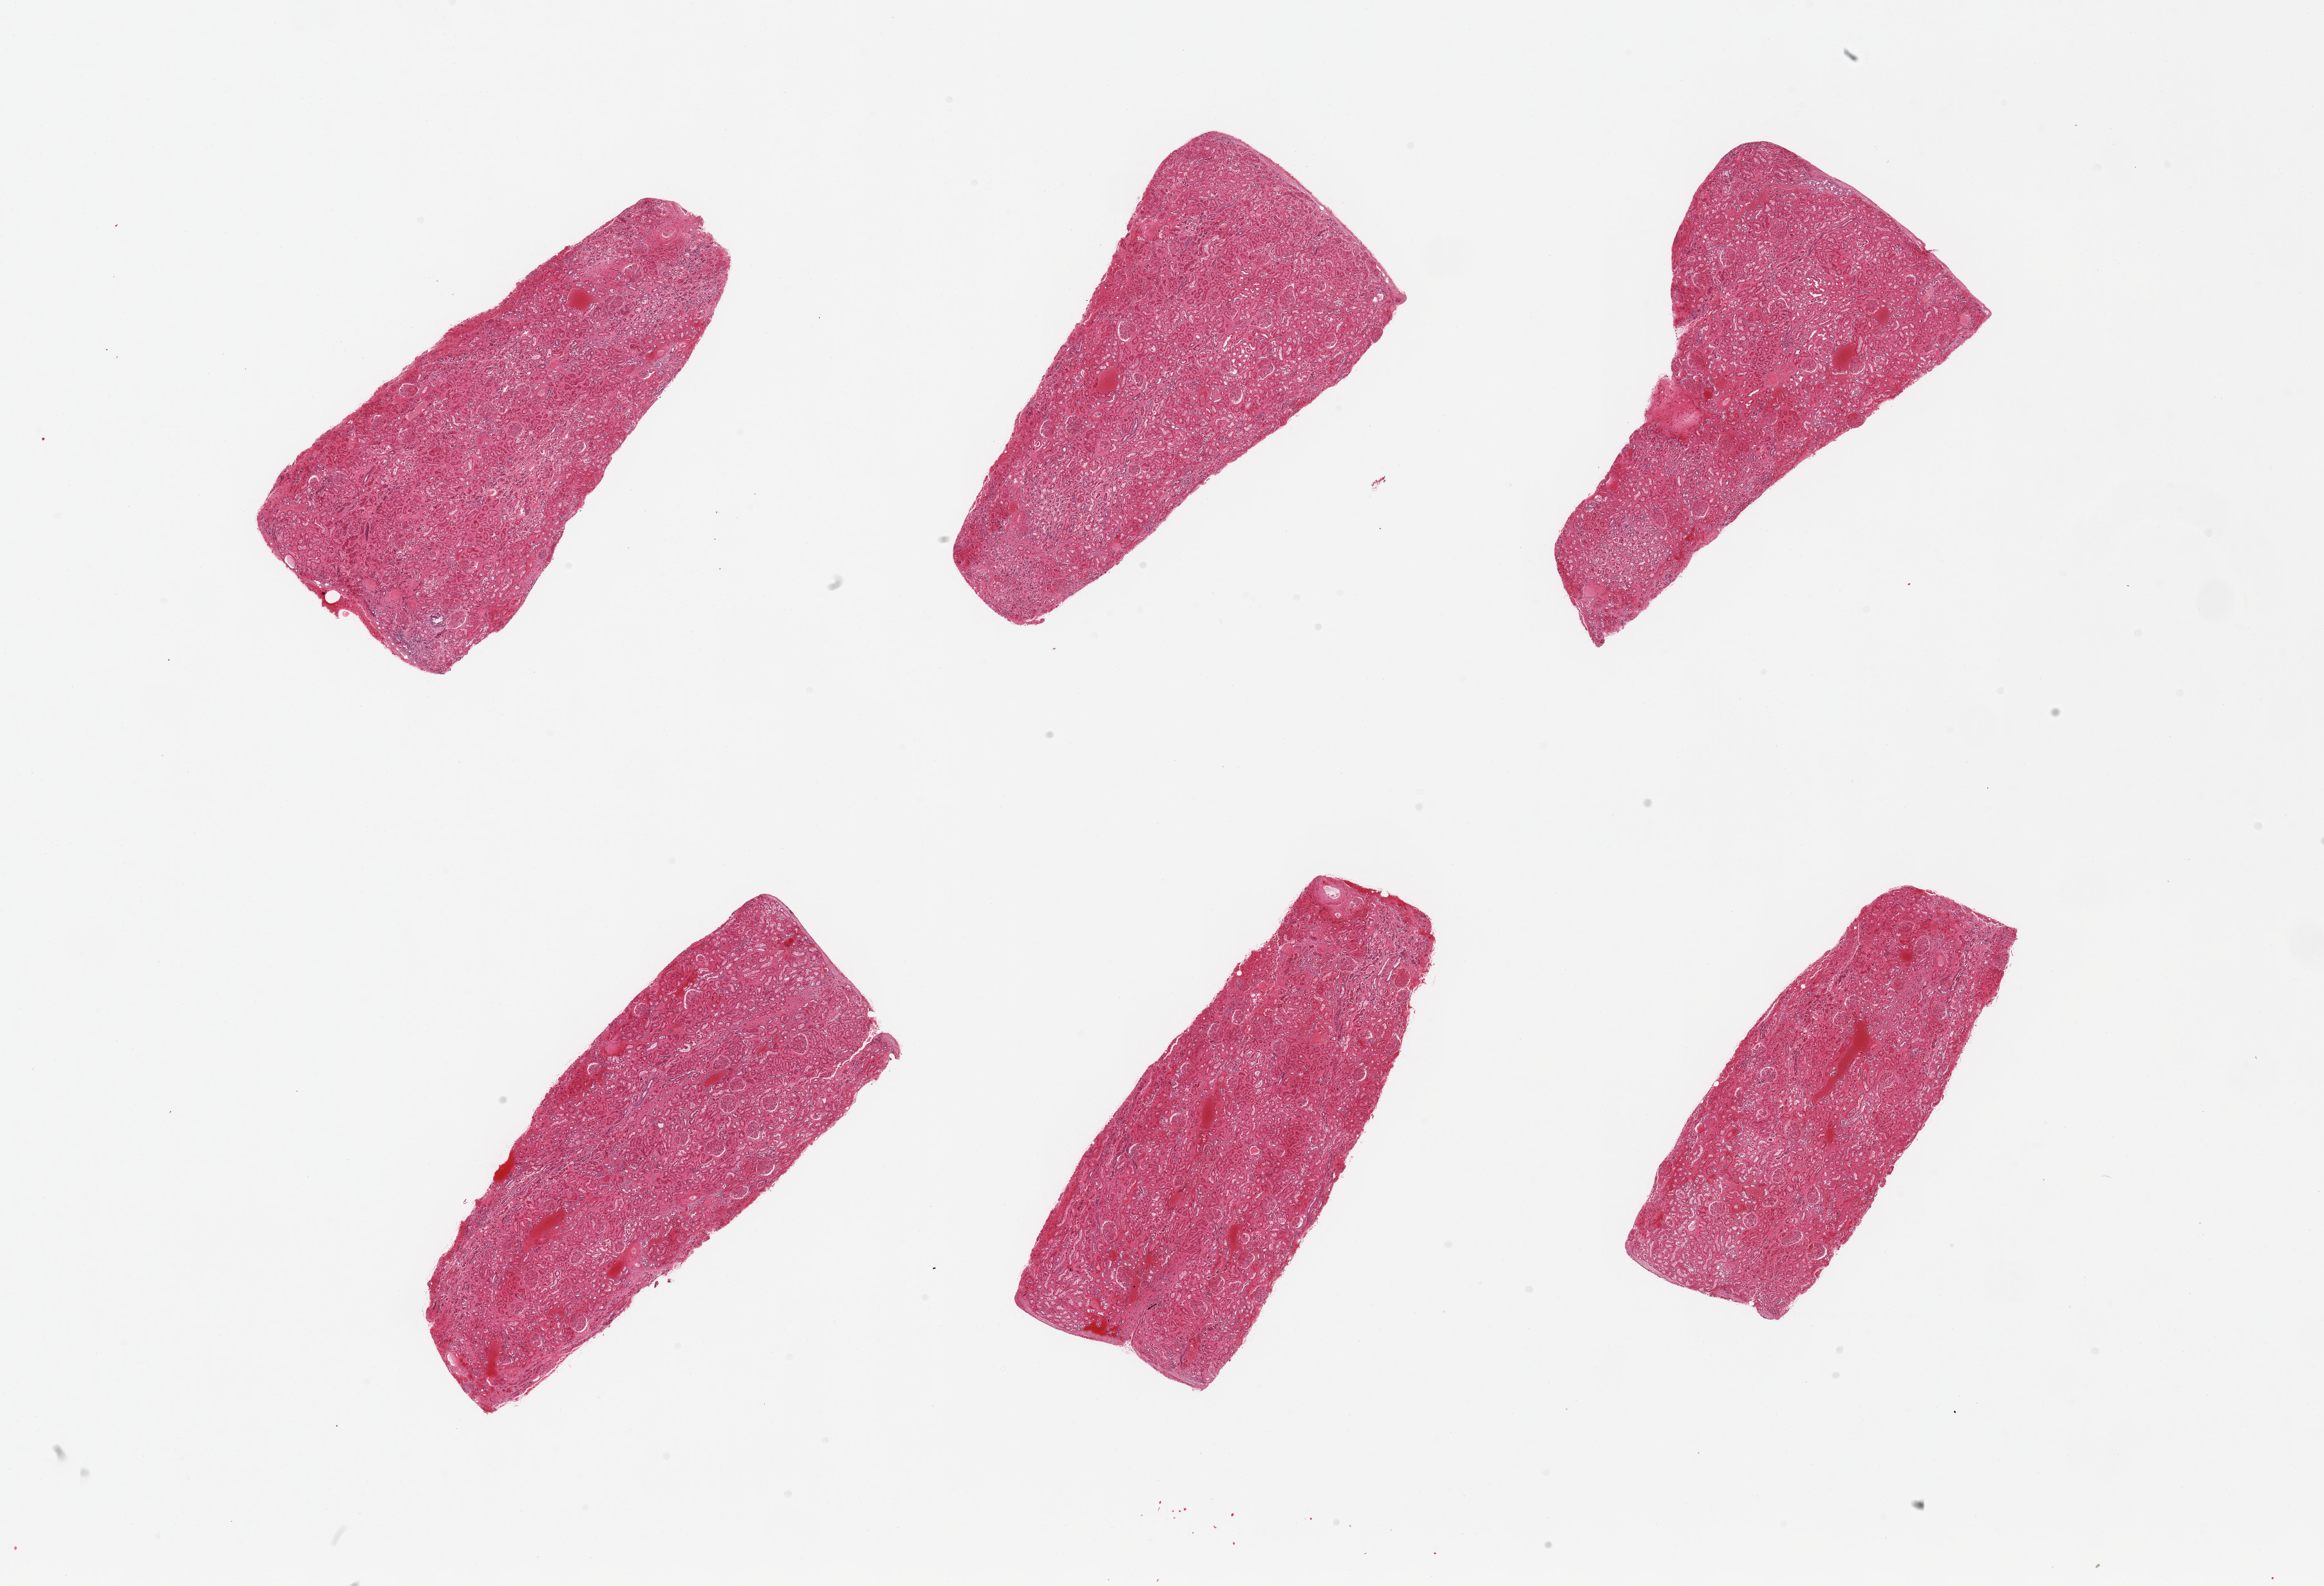
Digitized hematoxylin and eosin (H&E)-stained section — a low-resolution overview of the entire scanned area, about 28.5 x 19.5 mm (acquisition: 20x scan), PAXgene-fixed, paraffin-embedded tissue, section of renal cortex (target tissue), tissue donor sample. Donor: male.
• pathologist's review note for this sample: 6 pieces, glomeruli present, tubules autolyzed